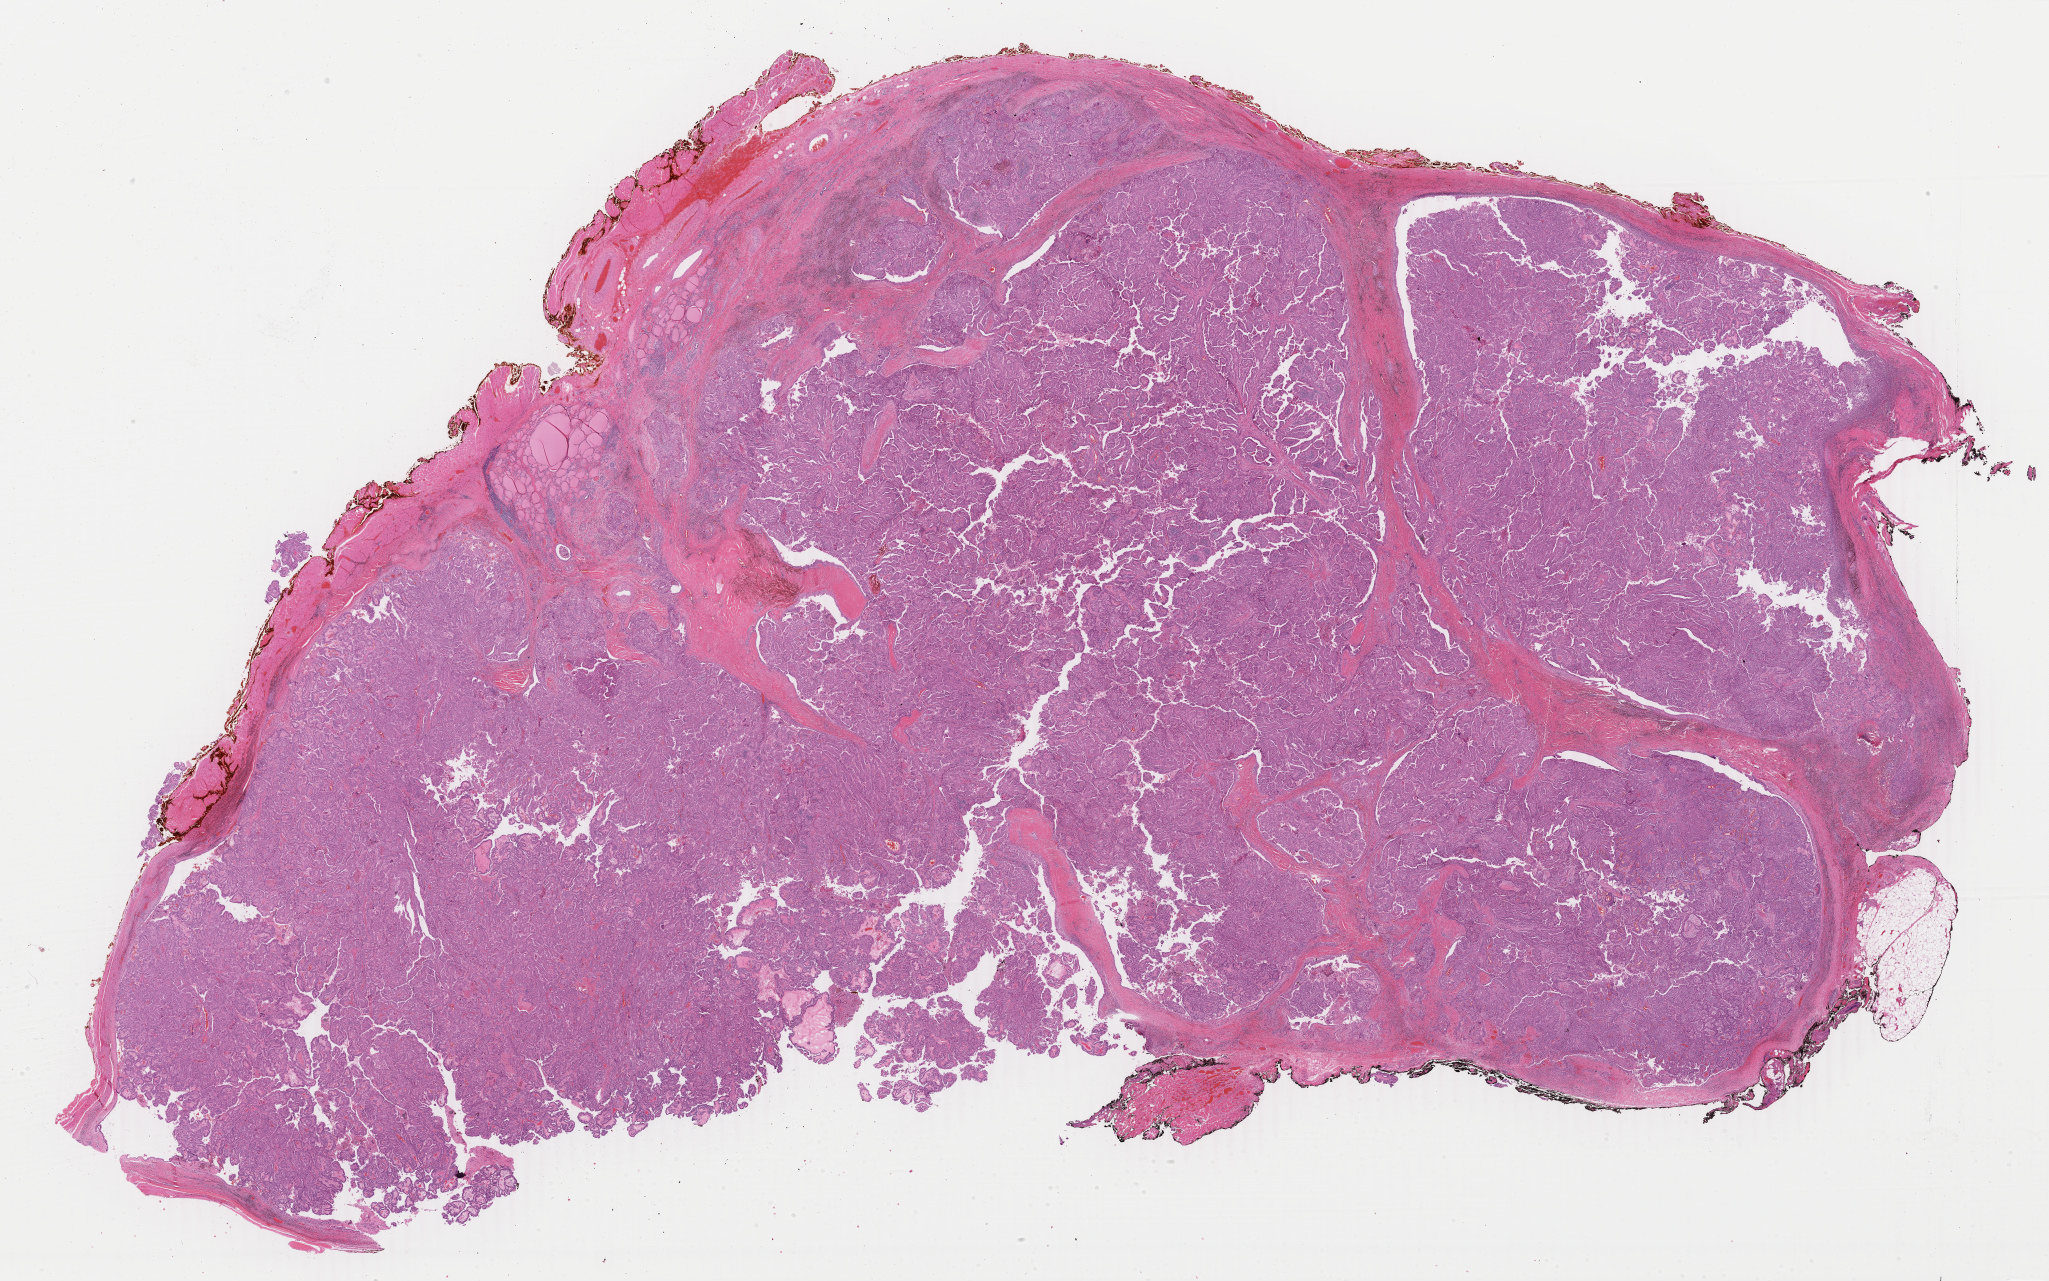
Whole-slide histology image, H&E, shown as a low-resolution overview of the whole scanned area (about 32.6 x 20.4 mm). Formalin-fixed paraffin-embedded (FFPE) diagnostic section. Sample: primary tumour, thyroid. Female patient; age at initial diagnosis 56 years.
Pathologic diagnosis: Papillary carcinoma, columnar cell (thyroid gland). TNM: T3 N0 MX. AJCC pathologic stage: III (6th edition).